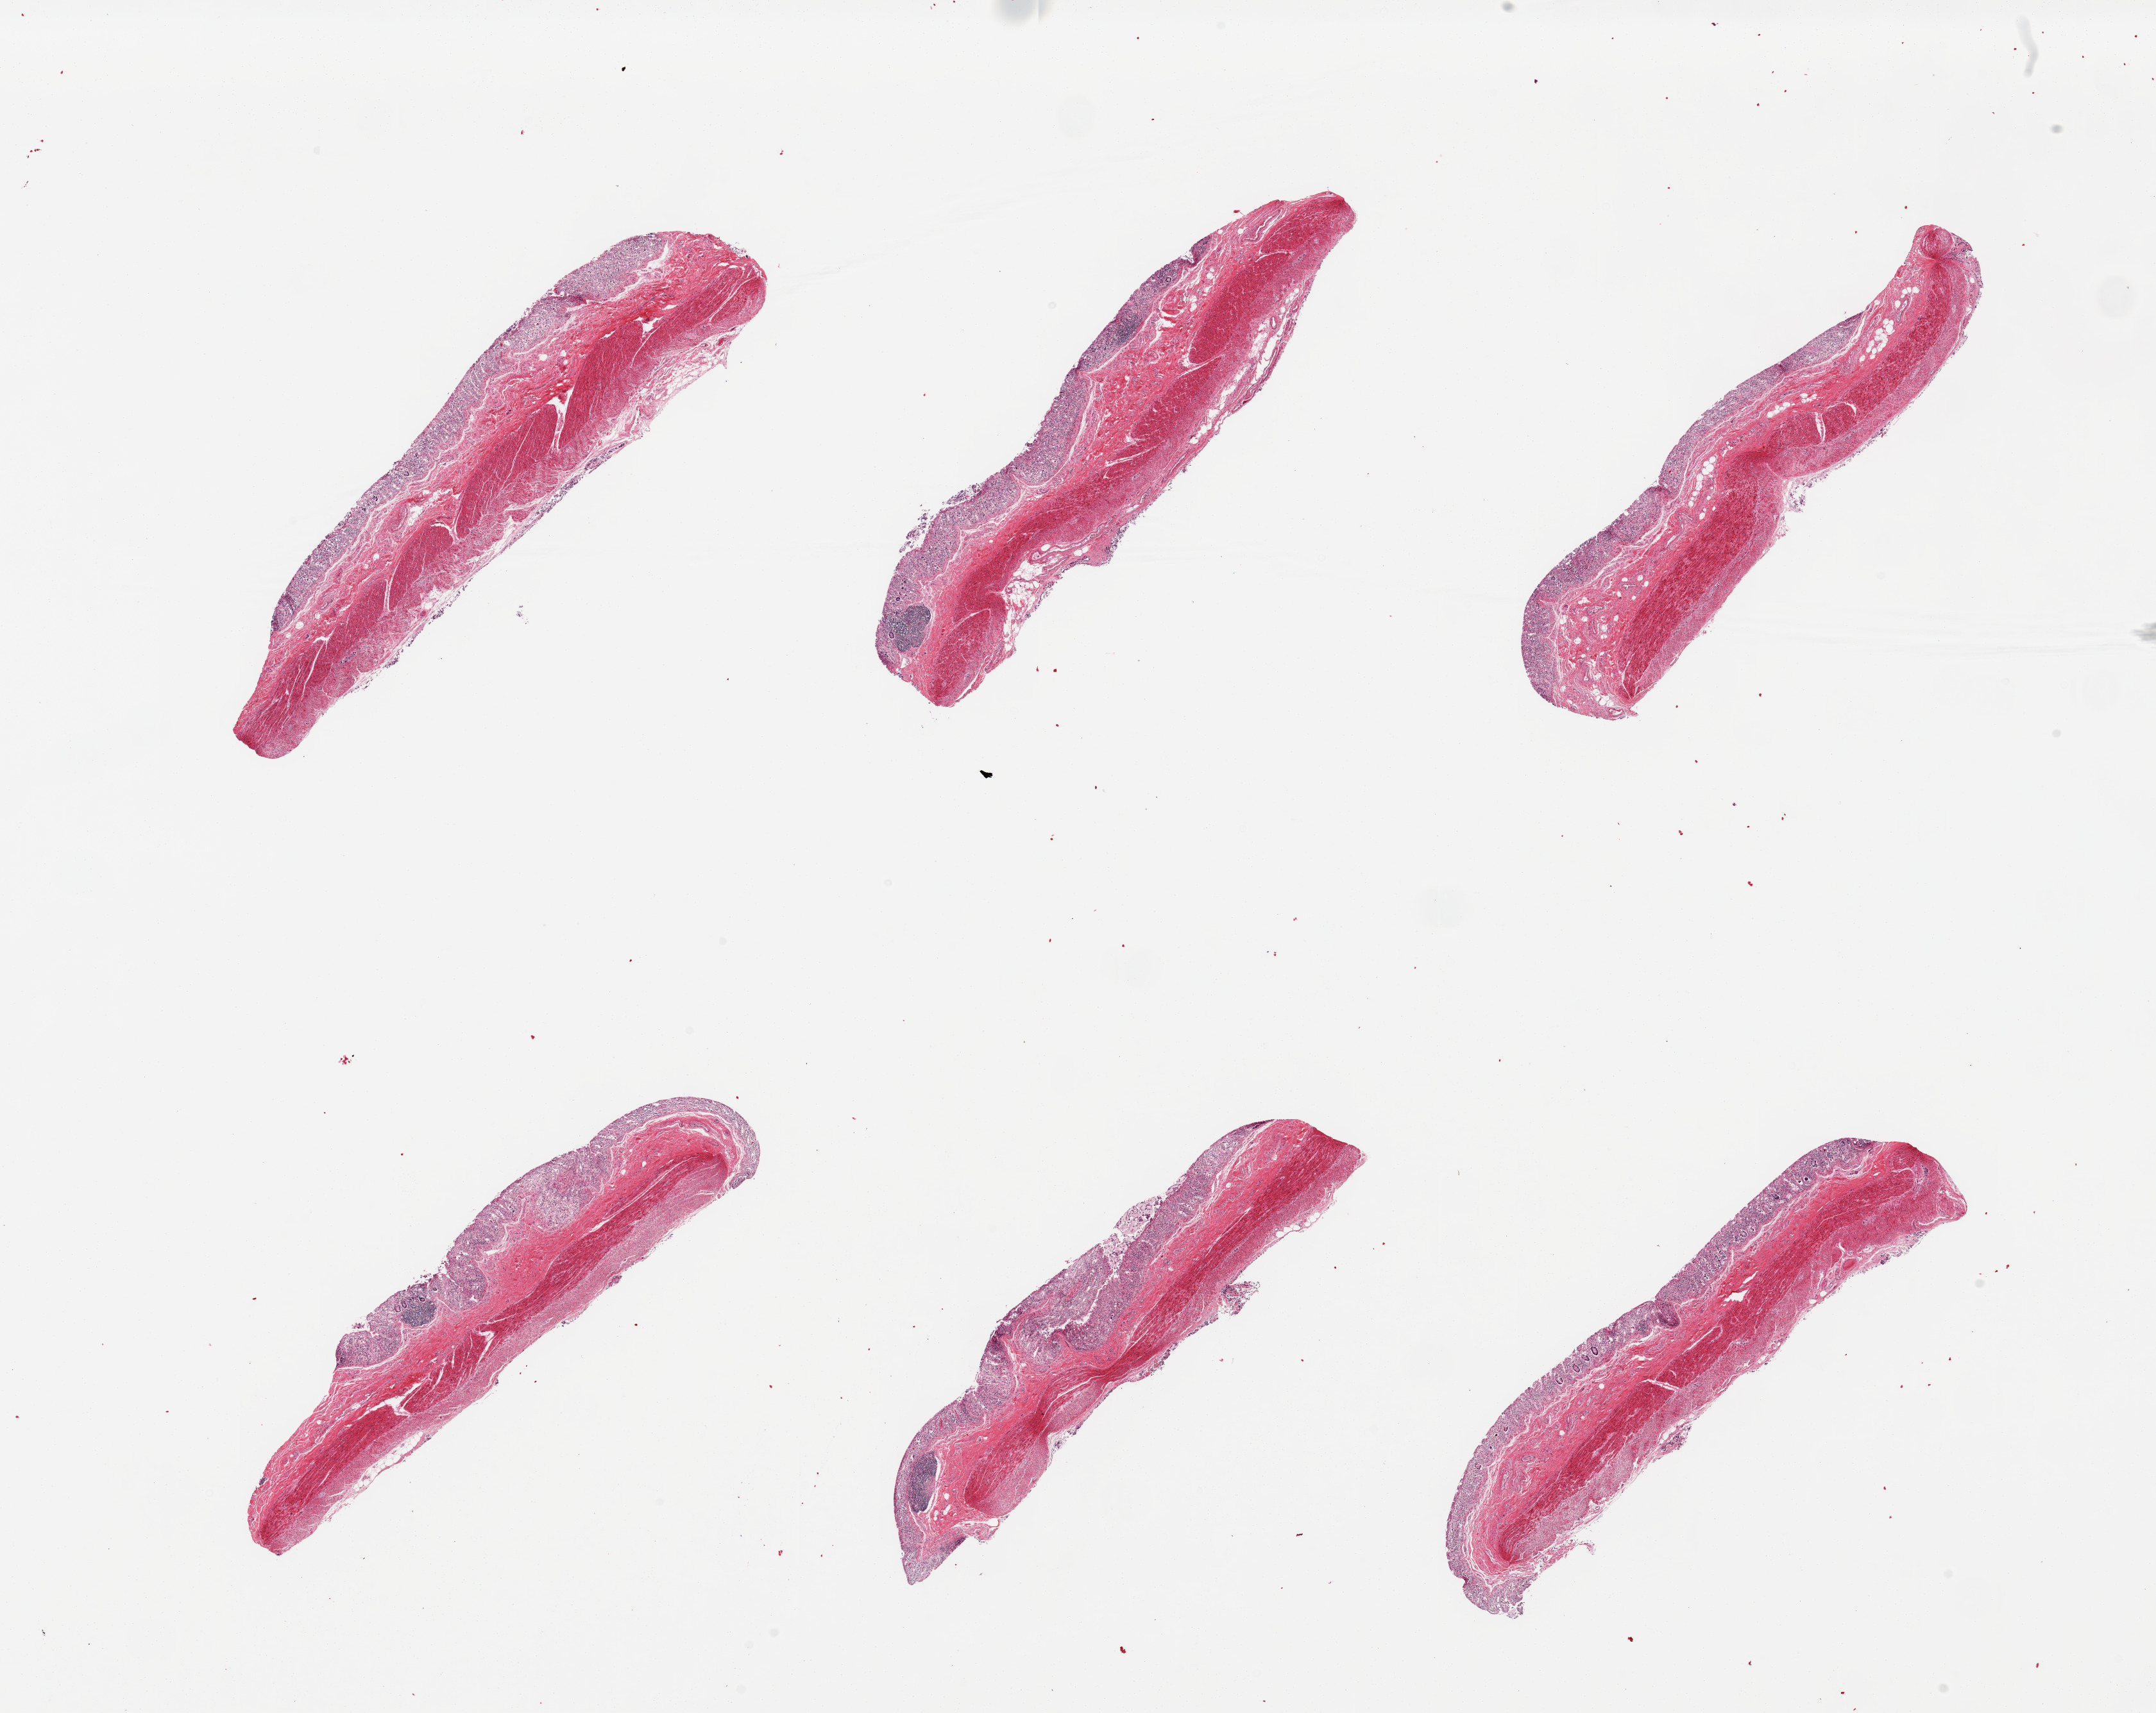
Hematoxylin and eosin (H&E) whole-slide image, low-resolution overview of the scanned area, about 26.6 x 21.1 mm. PAXgene-fixed, paraffin-embedded tissue. Sampled site (target tissue): transverse colon. Tissue donor sample. Donor sex: female.
• pathologist's review note for this sample: 6 pieces, muscularis and severely autolyzed mucosa